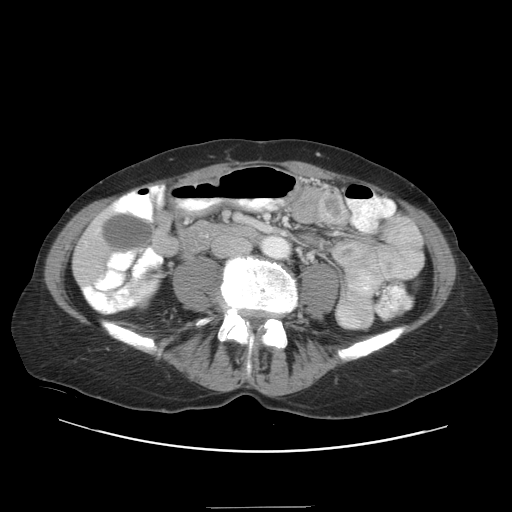
Contrast-enhanced abdominal CT, one axial slice. Position 3 of 38 along the scan axis. Reconstruction kernel STANDARD. 120 kVp. Intravenous contrast given. Soft-tissue window (W 400 / L 40 HU). 5 mm slice thickness. 512 × 512 image matrix, field of view 388 × 388 mm. Female patient, age 64 years. Case-level facts recorded for this patient, not image findings: diagnosis: colorectal cancer liver metastases, imaged before liver resection.
Structures marked on this image (manually delineated by an expert):
- liver: bounding box (x1, y1, x2, y2) in pixels: (75, 222, 106, 282)